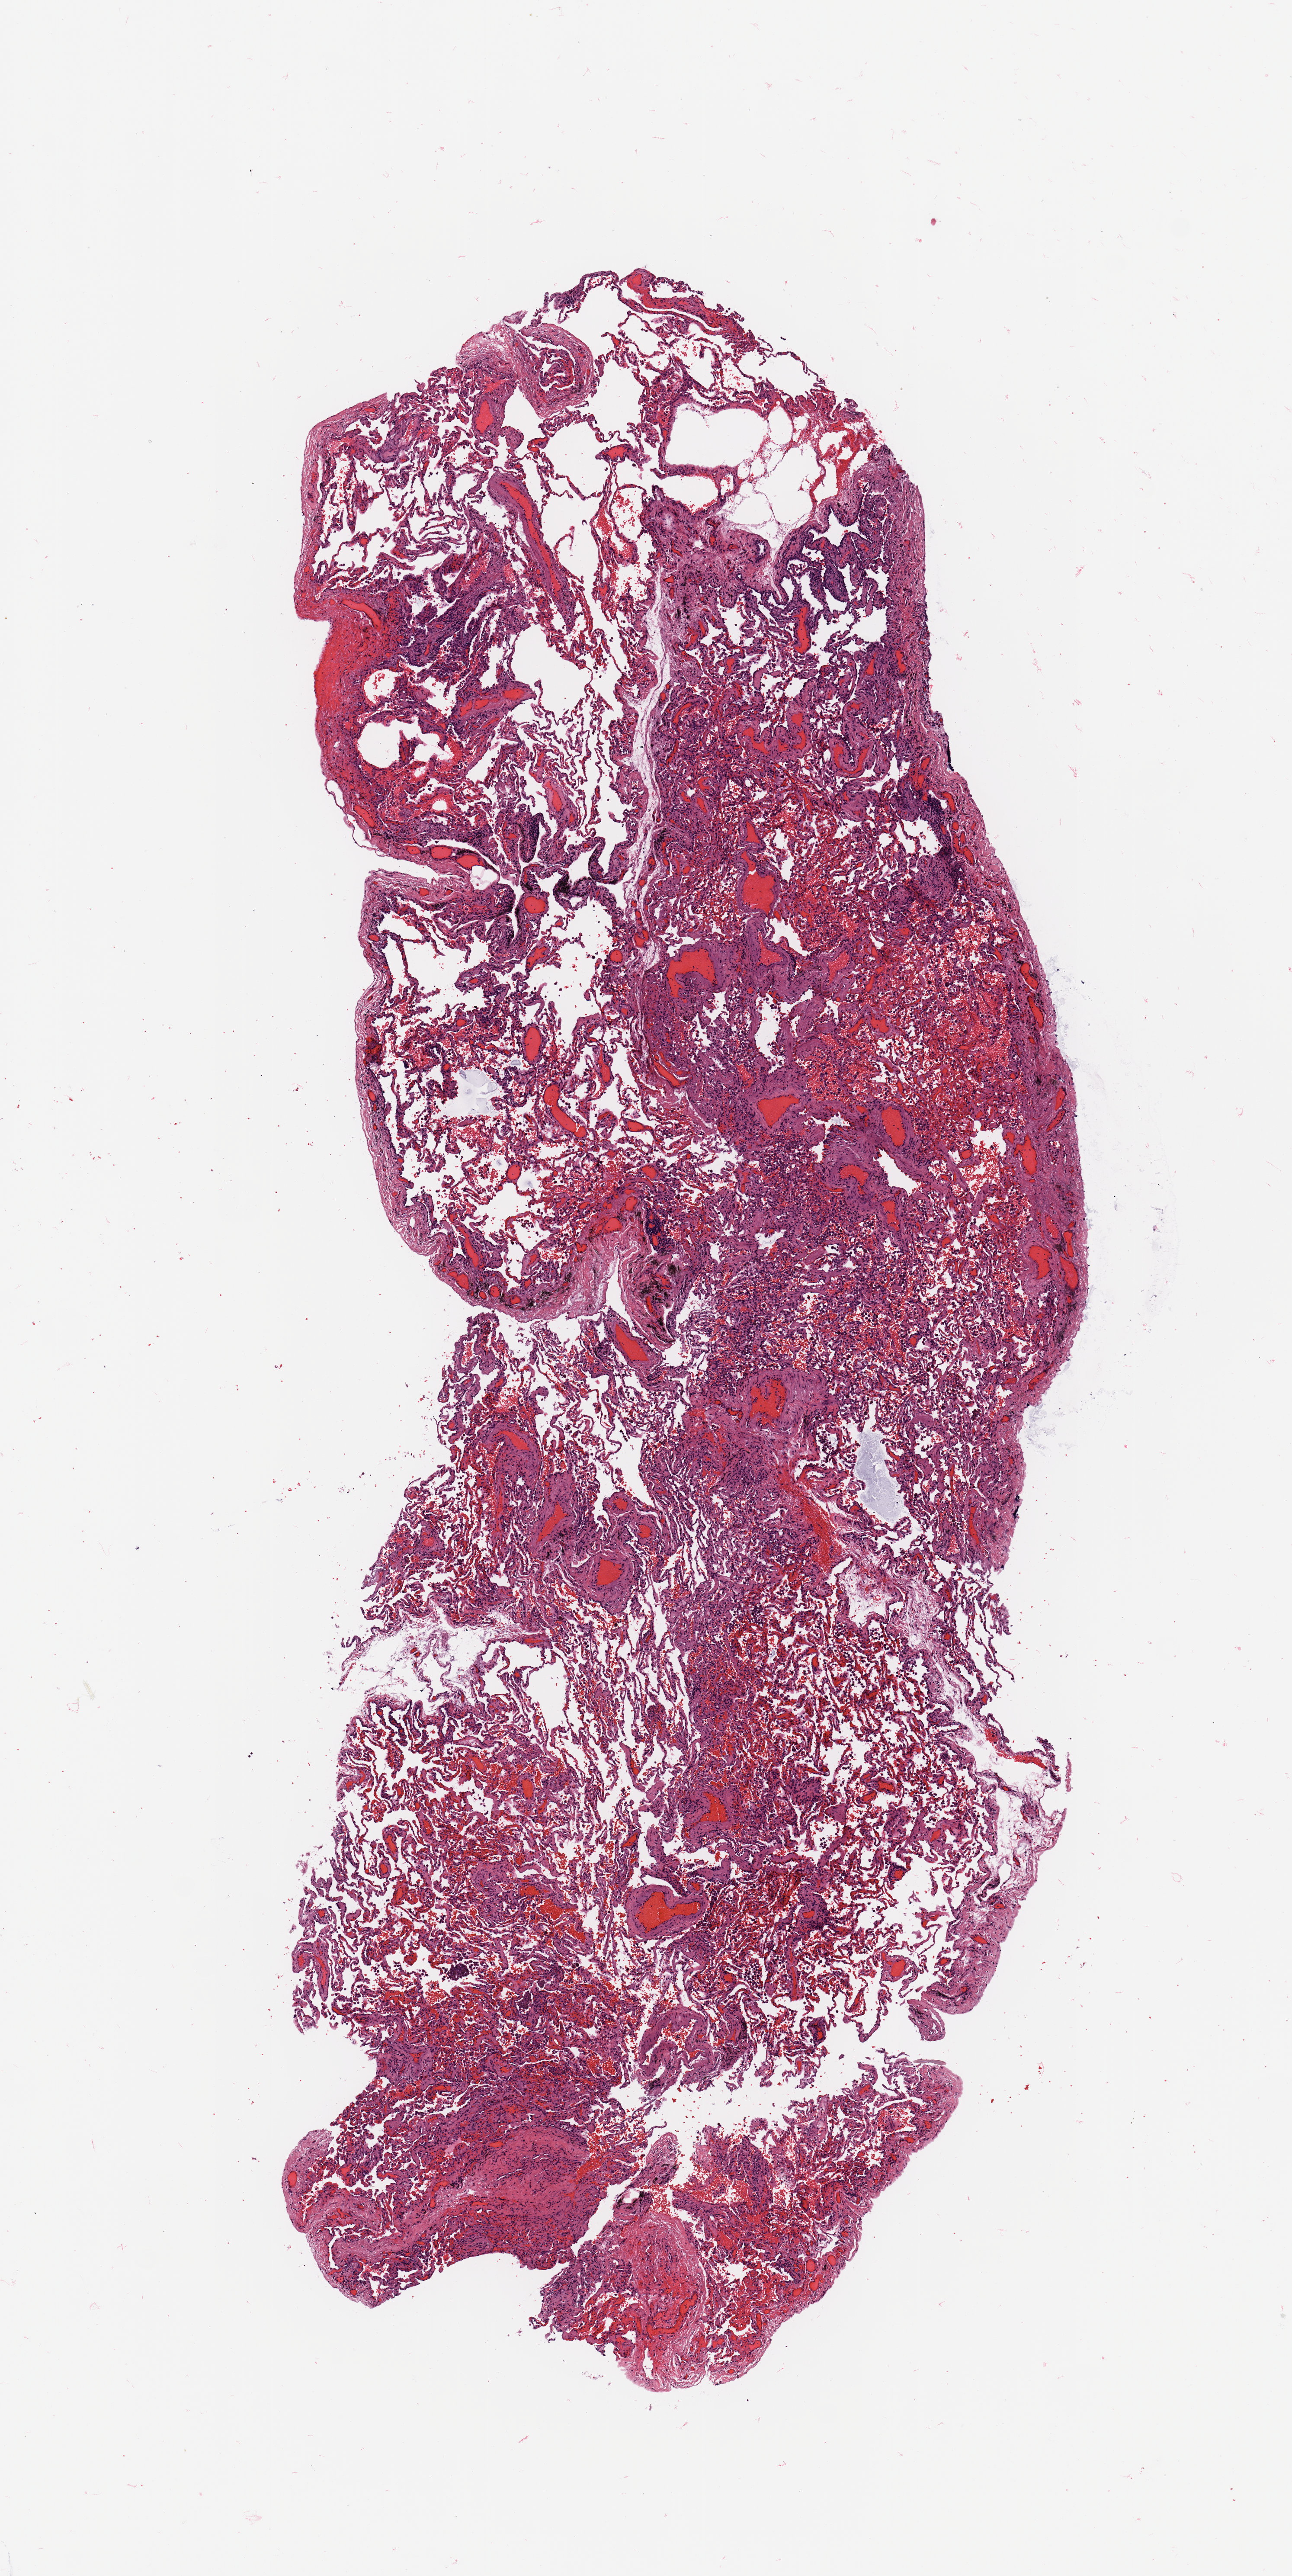
H&E whole-slide image, a low-resolution overview of the entire scanned area, about 5.9 x 11.8 mm (acquisition: 20x scan); normal (non-tumour) tissue sample, lung. Male, 71 y/o.
This section: normal (non-tumour) tissue from the same patient. Patient diagnosis: Adenocarcinoma, NOS.